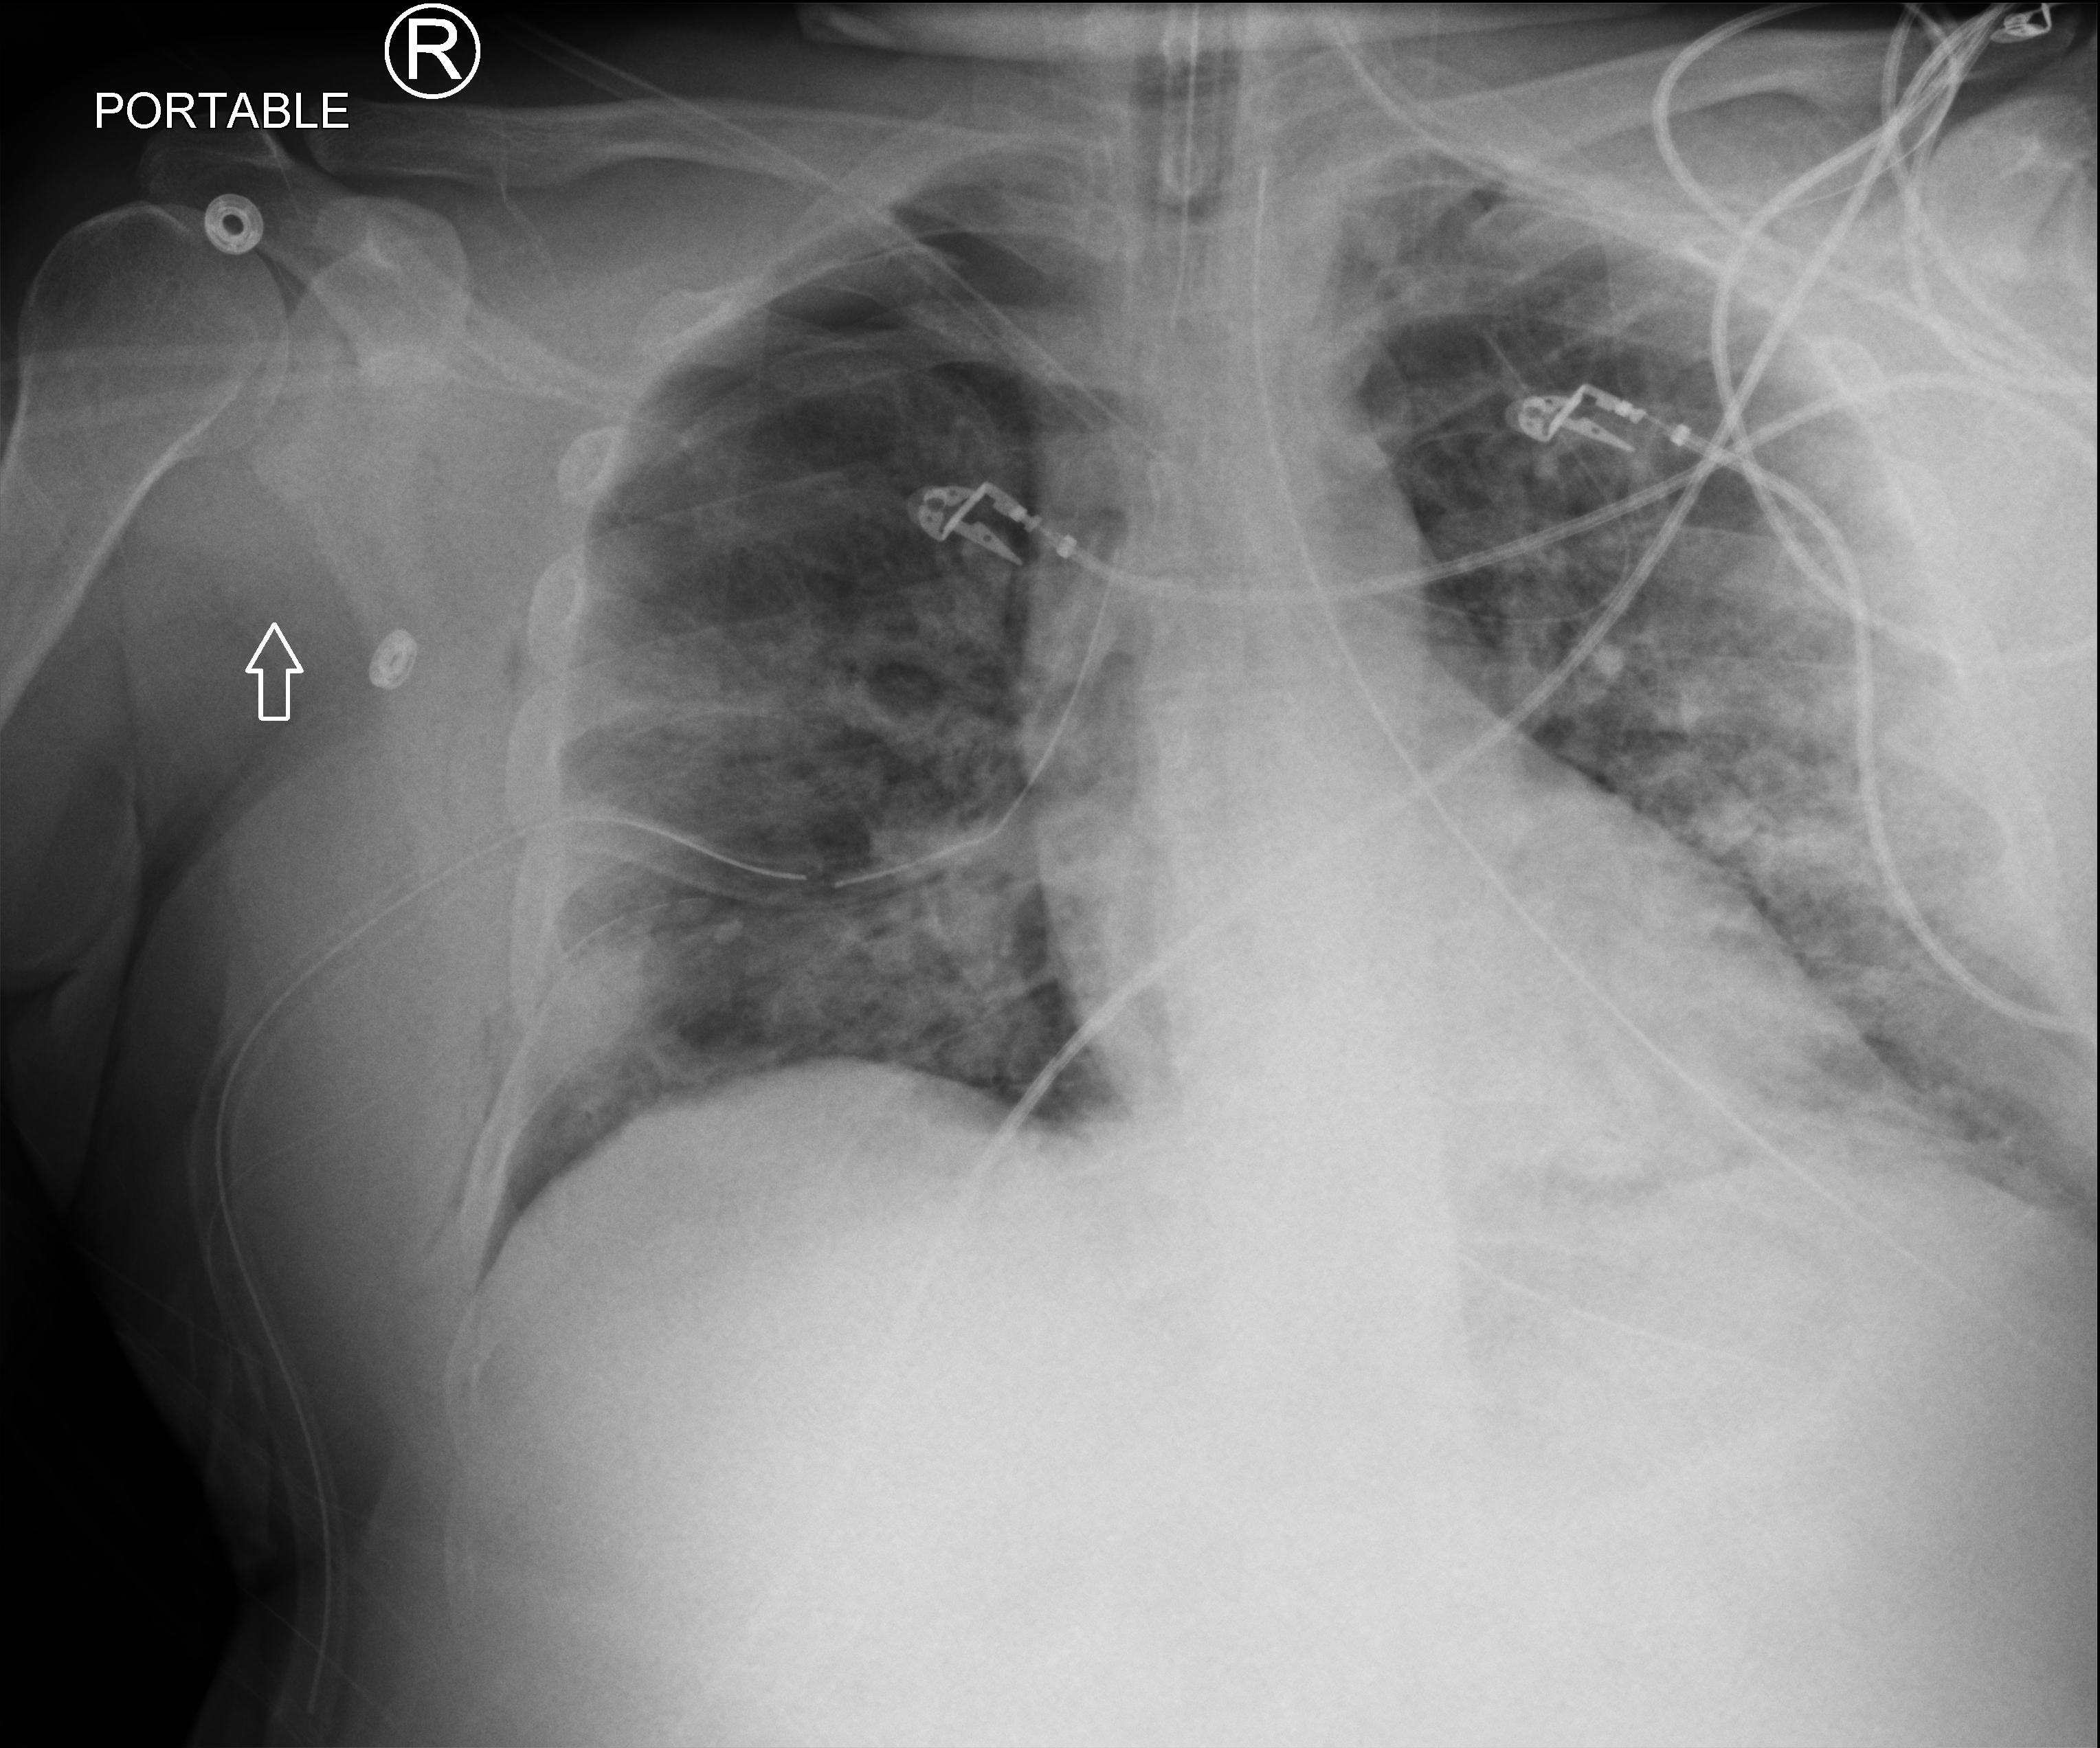
Chest X-ray (portable), anteroposterior (AP) projection. Patient hospitalised with COVID-19; male, aged 18–59 years.
Hospital-stay facts (about this admission, not read from this image; timing relative to this image not recorded): smoking status (admission record): never; admitted to intensive care during this hospital stay: yes.